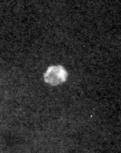
Crop from a digitized film mammogram around one marked abnormality; left breast; CC view; BI-RADS breast density category 1 (scale 1–4).
Finding: calcifications, morphology lucent centered; BI-RADS assessment category 2; benign without callback (not worked up further).